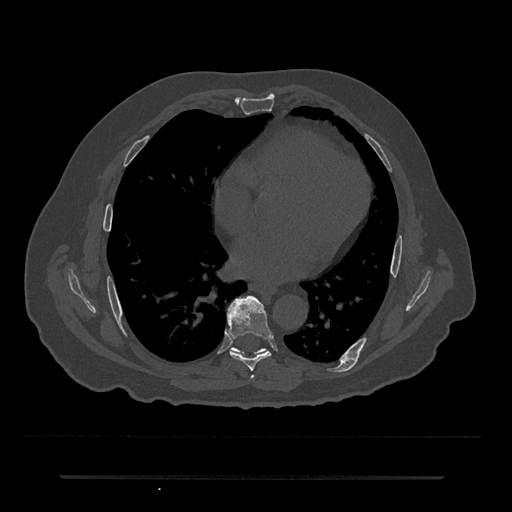
CT including the spine, one axial slice; slice 371 of 797 in the series (ordered by position); bone window (W 1800 / L 400 HU); 0.5 mm slice thickness; 512 × 512 image matrix, field of view 437 × 437 mm. Patient: male, 69 years. From the clinical record (not read from this slice): primary cancer: prostate.
Annotated regions visible in this slice (semi-automatic segmentation, software-assisted and operator-edited):
- T6 vertebra: bounding box <251,376,254,379> (left, top, right, bottom; pixels)
- T7 vertebra: <227,295,272,371>
- T8 vertebra: <230,347,266,355>